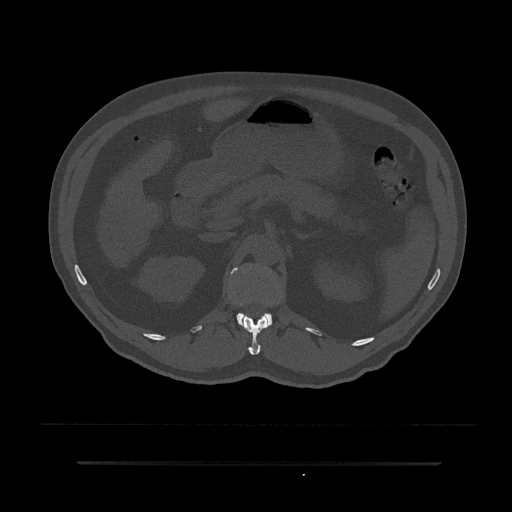
CT including the spine, one axial slice. Slice 181 of 797 in the series (ordered by position). Reconstruction kernel Br40s/3. Bone window (W 1800 / L 400 HU). 0.5 mm slice thickness. 512 × 512 image matrix, field of view 464 × 464 mm. Male patient, age 59 years. From the clinical record (not read from this slice): primary cancer: bile ducts.
Structures marked on this image (semi-automatic segmentation, software-assisted and operator-edited):
- L1 vertebra: box from (x=231, y=267) to (x=272, y=325) px
- T12 vertebra: (x=241, y=314)–(x=269, y=355)